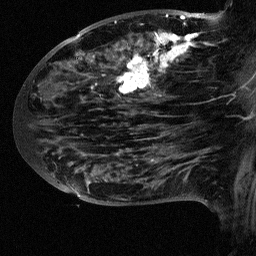
Breast MRI (dynamic contrast-enhanced), one sagittal slice; position 32 of 64 along the scan axis; dynamic contrast-enhanced study with each time point stored as its own series, time point 2 of 3 at this slice position (early post-contrast, ordered by acquisition time); 1.5 T; TE 4.5 ms, TR 11 ms; 256 × 256 image matrix, field of view 200 × 200 mm. Patient: female, 38 years. From the clinical record (not read from this slice): setting: breast cancer imaged before/during neoadjuvant chemotherapy; receptor status: HR-positive, HER2-negative.
Structures marked on this image (semi-automatically segmented with operator editing):
- analysis volume of interest (the breast-tissue region the enhancement analysis was run in; not a lesion): bounding box (x1, y1, x2, y2) in pixels: (88, 18, 252, 126)
- tumour enhancement mask (voxels above the 90 % enhancement threshold inside the analysis volume of interest): (92, 18, 251, 117)